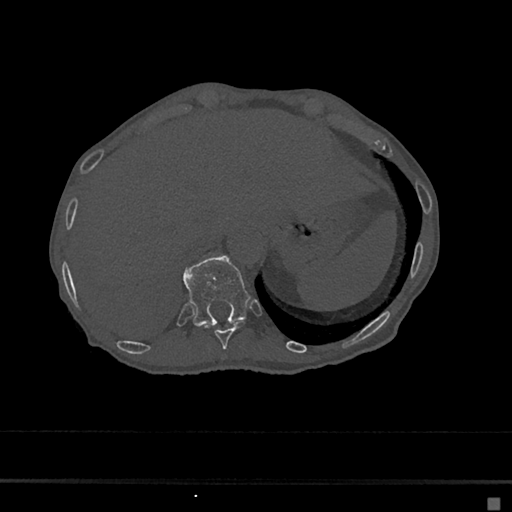
CT including the spine, one axial slice; slice 192 of 797 in the series (ordered by position); reconstruction kernel Br40s/3; bone window (W 1800 / L 400 HU); 0.5 mm slice thickness; 512 × 512 image matrix. Patient: female, 68 years. From the clinical record (not read from this slice): primary cancer: renal.
Outlined on this slice (semi-automatic segmentation, software-assisted and operator-edited):
- T10 vertebra: box from (x=204, y=322) to (x=245, y=349) px
- T11 vertebra: (x=184, y=257)–(x=250, y=326)